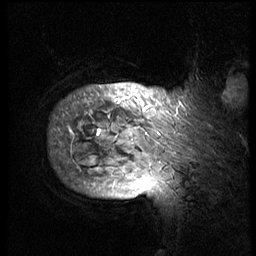
Breast MRI (dynamic contrast-enhanced), one sagittal slice; slice 65 of 74 in the series (ordered by position); 3 images stored at this slice position (order not interpretable as contrast timing); 1.5 T; TE 4.2 ms, TR 8.9 ms; 2.5 mm slice thickness; 256 × 256 image matrix, field of view 200 × 200 mm. Patient: female, 57 years. Case-level facts recorded for this patient, not image findings: setting: breast cancer imaged before/during neoadjuvant chemotherapy; receptor status: HER2-positive.
Structures marked on this image (semi-automatic segmentation, software-assisted and operator-edited):
- analysis volume of interest (the breast-tissue region the enhancement analysis was run in; not a lesion): bounding box [x1, y1, x2, y2] px = [43, 62, 239, 175]
- tumour enhancement mask (voxels above the 140 % enhancement threshold inside the analysis volume of interest): [70, 92, 184, 175]